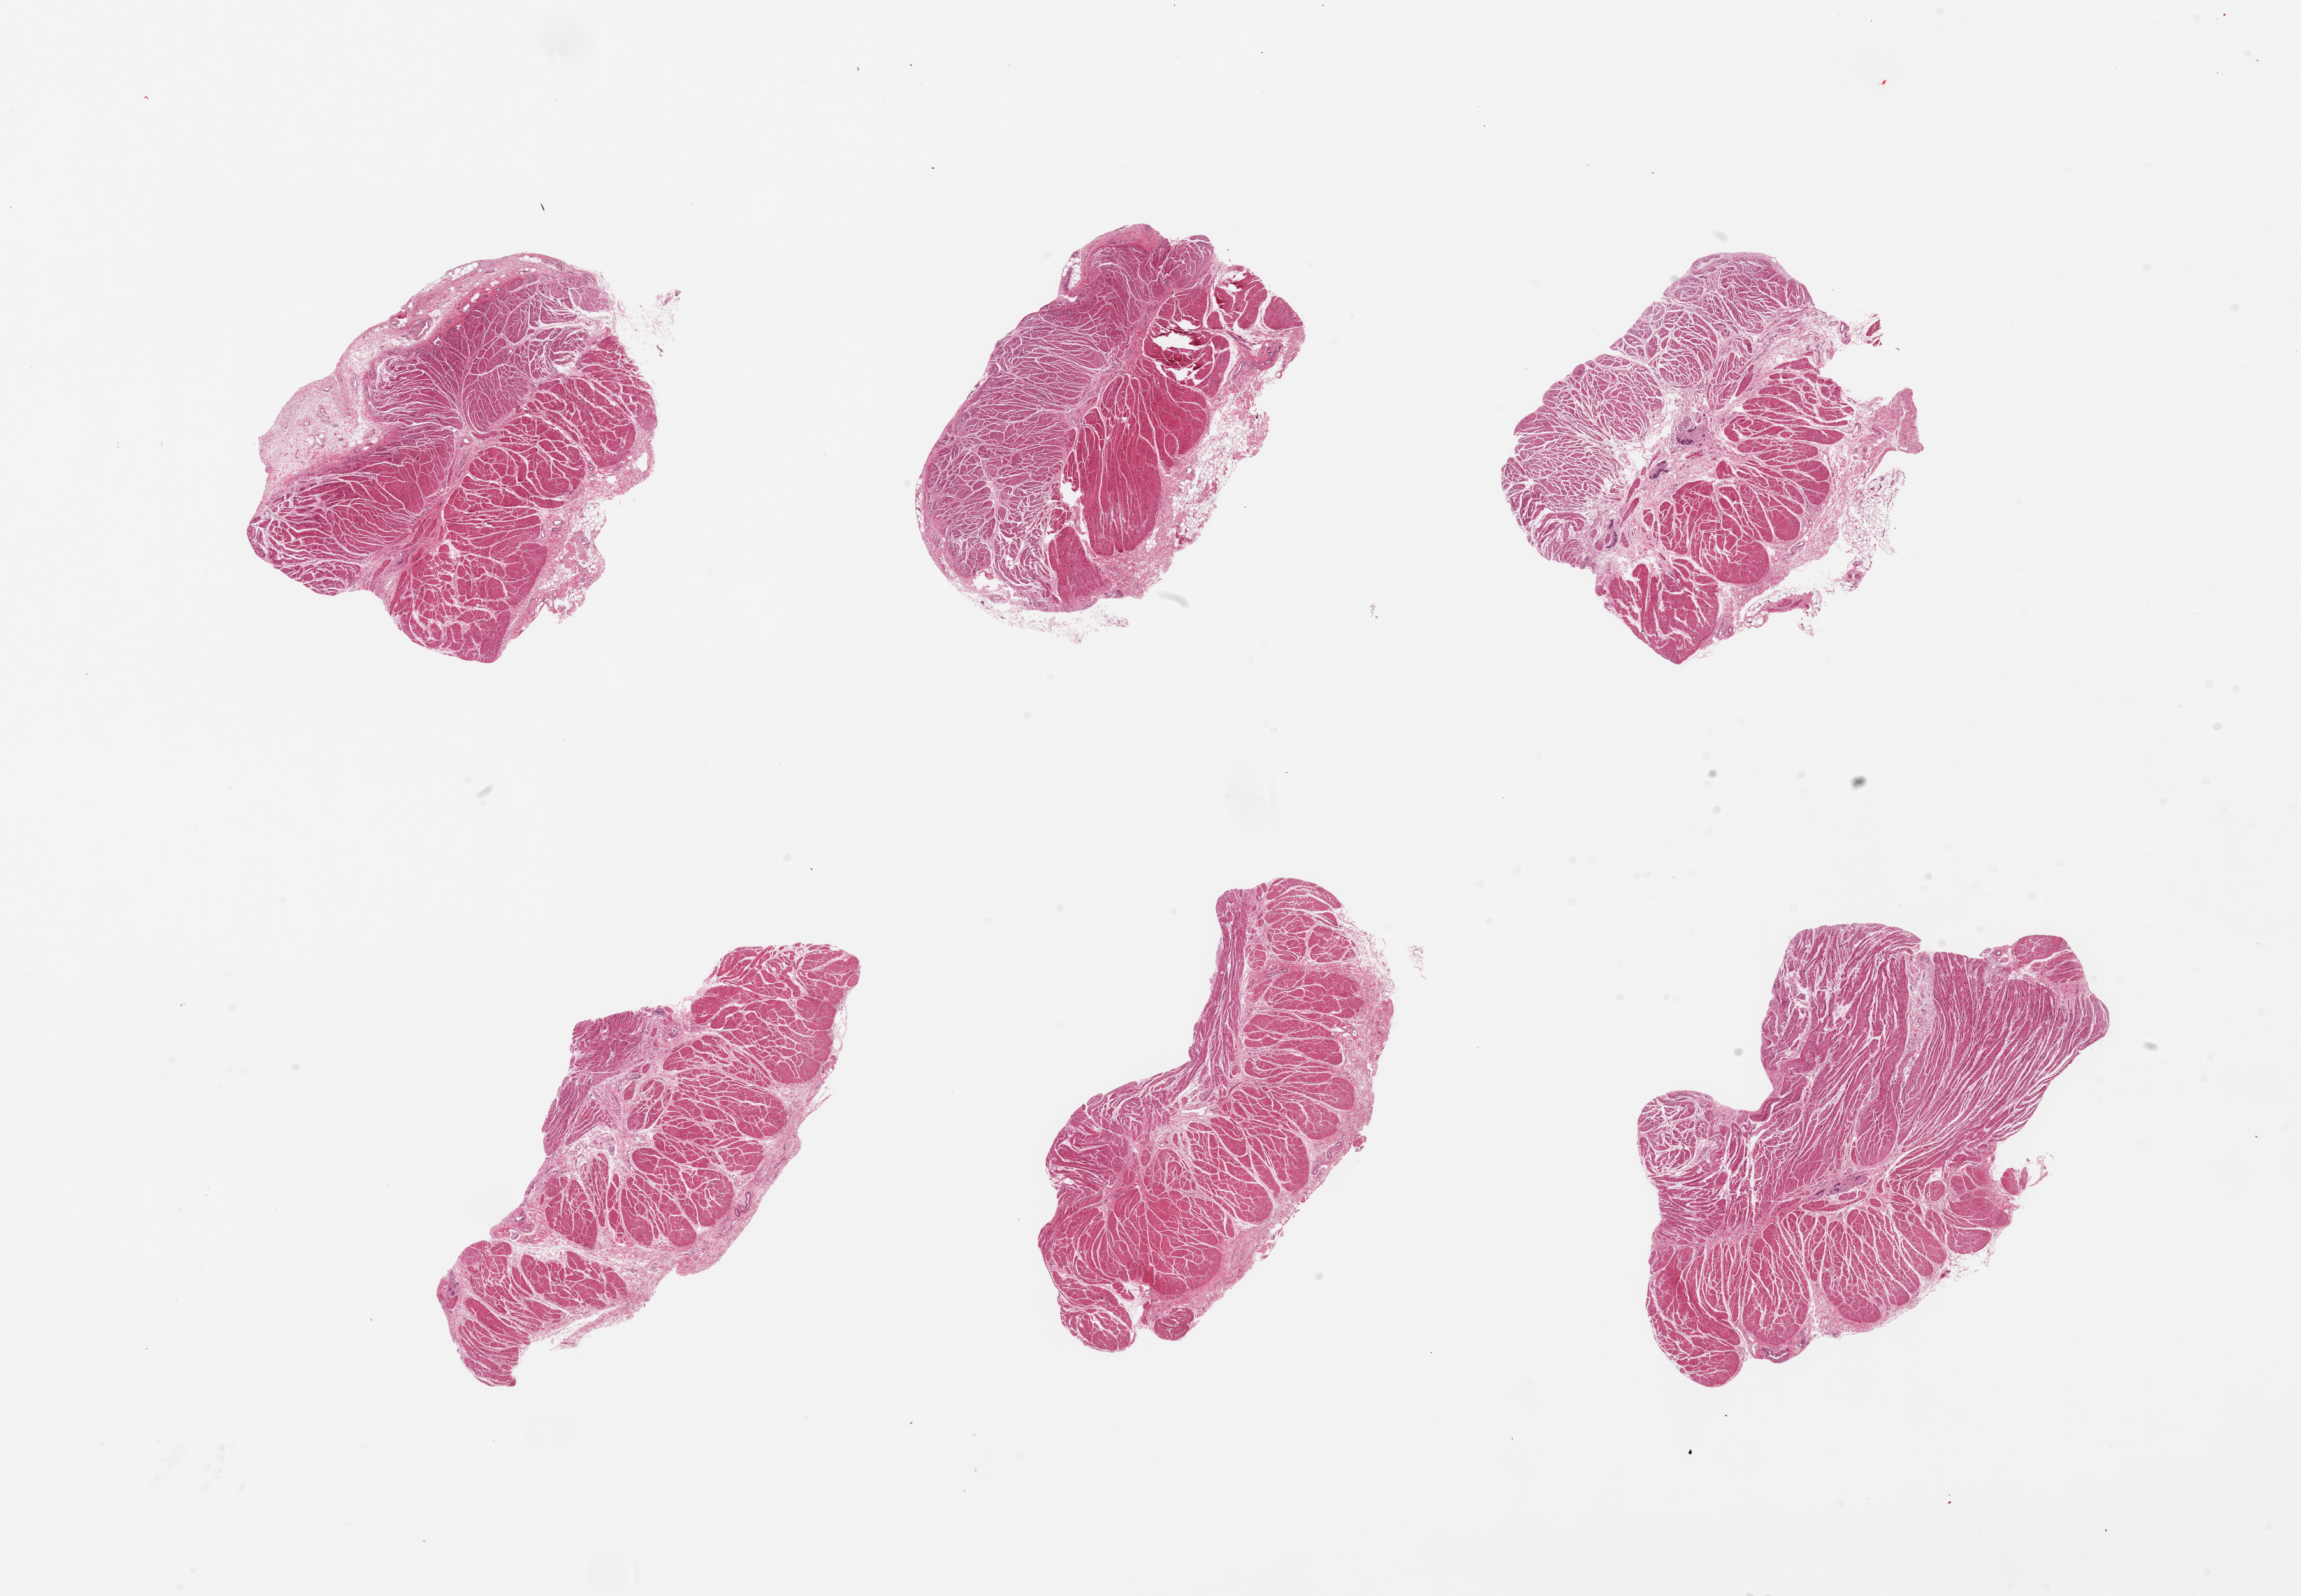
Hematoxylin and eosin (H&E) whole-slide image — shown as a low-resolution overview of the whole scanned area (about 28.5 x 19.8 mm). Male donor.
- specimen: PAXgene-fixed paraffin-embedded (PFPE) section; target tissue: gastroesophageal junction; donor tissue sample